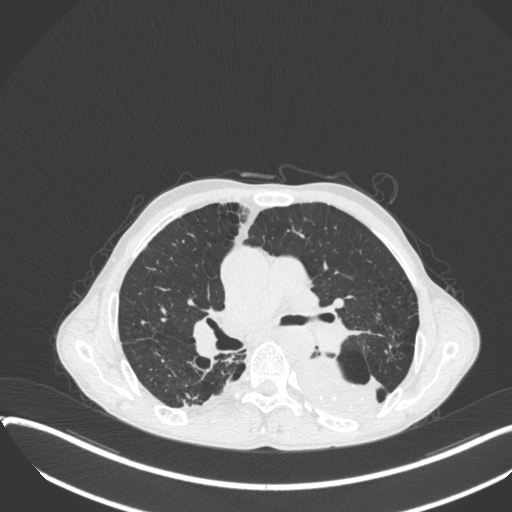
Chest CT, one axial slice; reconstruction kernel B31f; 120 kVp; lung window (W 1500 / L -600 HU); 1 mm slice thickness; 512 × 512 image matrix, field of view 400 × 400 mm. Male patient, age 57 years. Case-level facts recorded for this patient, not image findings: clinical TNM (as recorded): T4 N0 M0.
Outlined on this slice (bounding box drawn by a radiologist):
- lung tumour (recorded histology: squamous cell carcinoma): bounding box <291,349,382,423> (left, top, right, bottom; pixels)